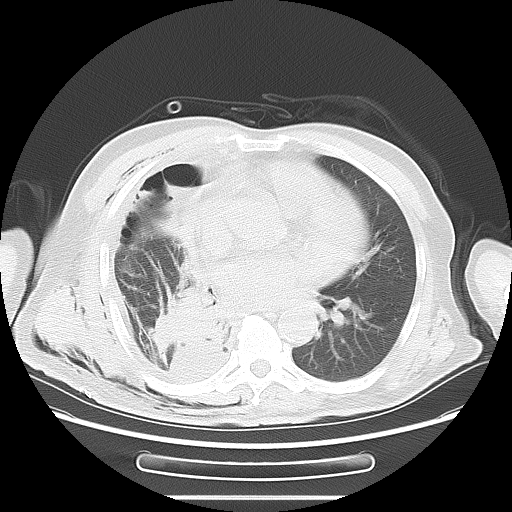
Chest CT, one axial slice. Slice 30 of 59 in the series (ordered by position). Lung window (W 1500 / L -600 HU). 5 mm slice thickness. 512 × 512 image matrix, field of view 392 × 392 mm. Male patient, age 69 years. From the clinical record (not read from this slice): clinical TNM (as recorded): T3 N0 M0.
Outlined on this slice (bounding box drawn by a radiologist):
- lung tumour (recorded histology: squamous cell carcinoma): box from (x=136, y=287) to (x=231, y=380) px